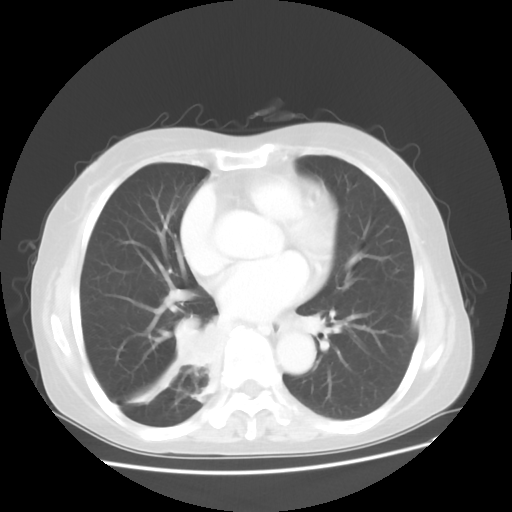
Chest CT, one axial slice; position 20 of 48 along the scan axis; 120 kVp; lung window (W 1500 / L -600 HU); 512 × 512 image matrix. Patient: female, 63 years. Case-level facts recorded for this patient, not image findings: clinical TNM (as recorded): T2 N3 M1b.
Structures marked on this image (rectangle marked by the reading radiologist):
- lung tumour (recorded histology: small cell carcinoma): bounding box [x1, y1, x2, y2] px = [168, 318, 221, 377]